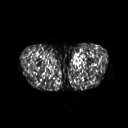
FDG PET of an extremity soft-tissue mass (from a PET/CT study), one axial slice; slice 255 of 311 in the series (ordered by position); 3.27 mm slice thickness; 128 × 128 image matrix. Male patient, age 29 years. From the clinical record (not read from this slice): histological type: mixoid liposarcoma; grade: low; site of the primary tumour: left thigh.
Structures marked on this image (expert contour drawn on MRI and transferred to this co-registered scan by the dataset authors):
- gross tumour volume (mass): bounding box [x1, y1, x2, y2] px = [71, 54, 83, 66]